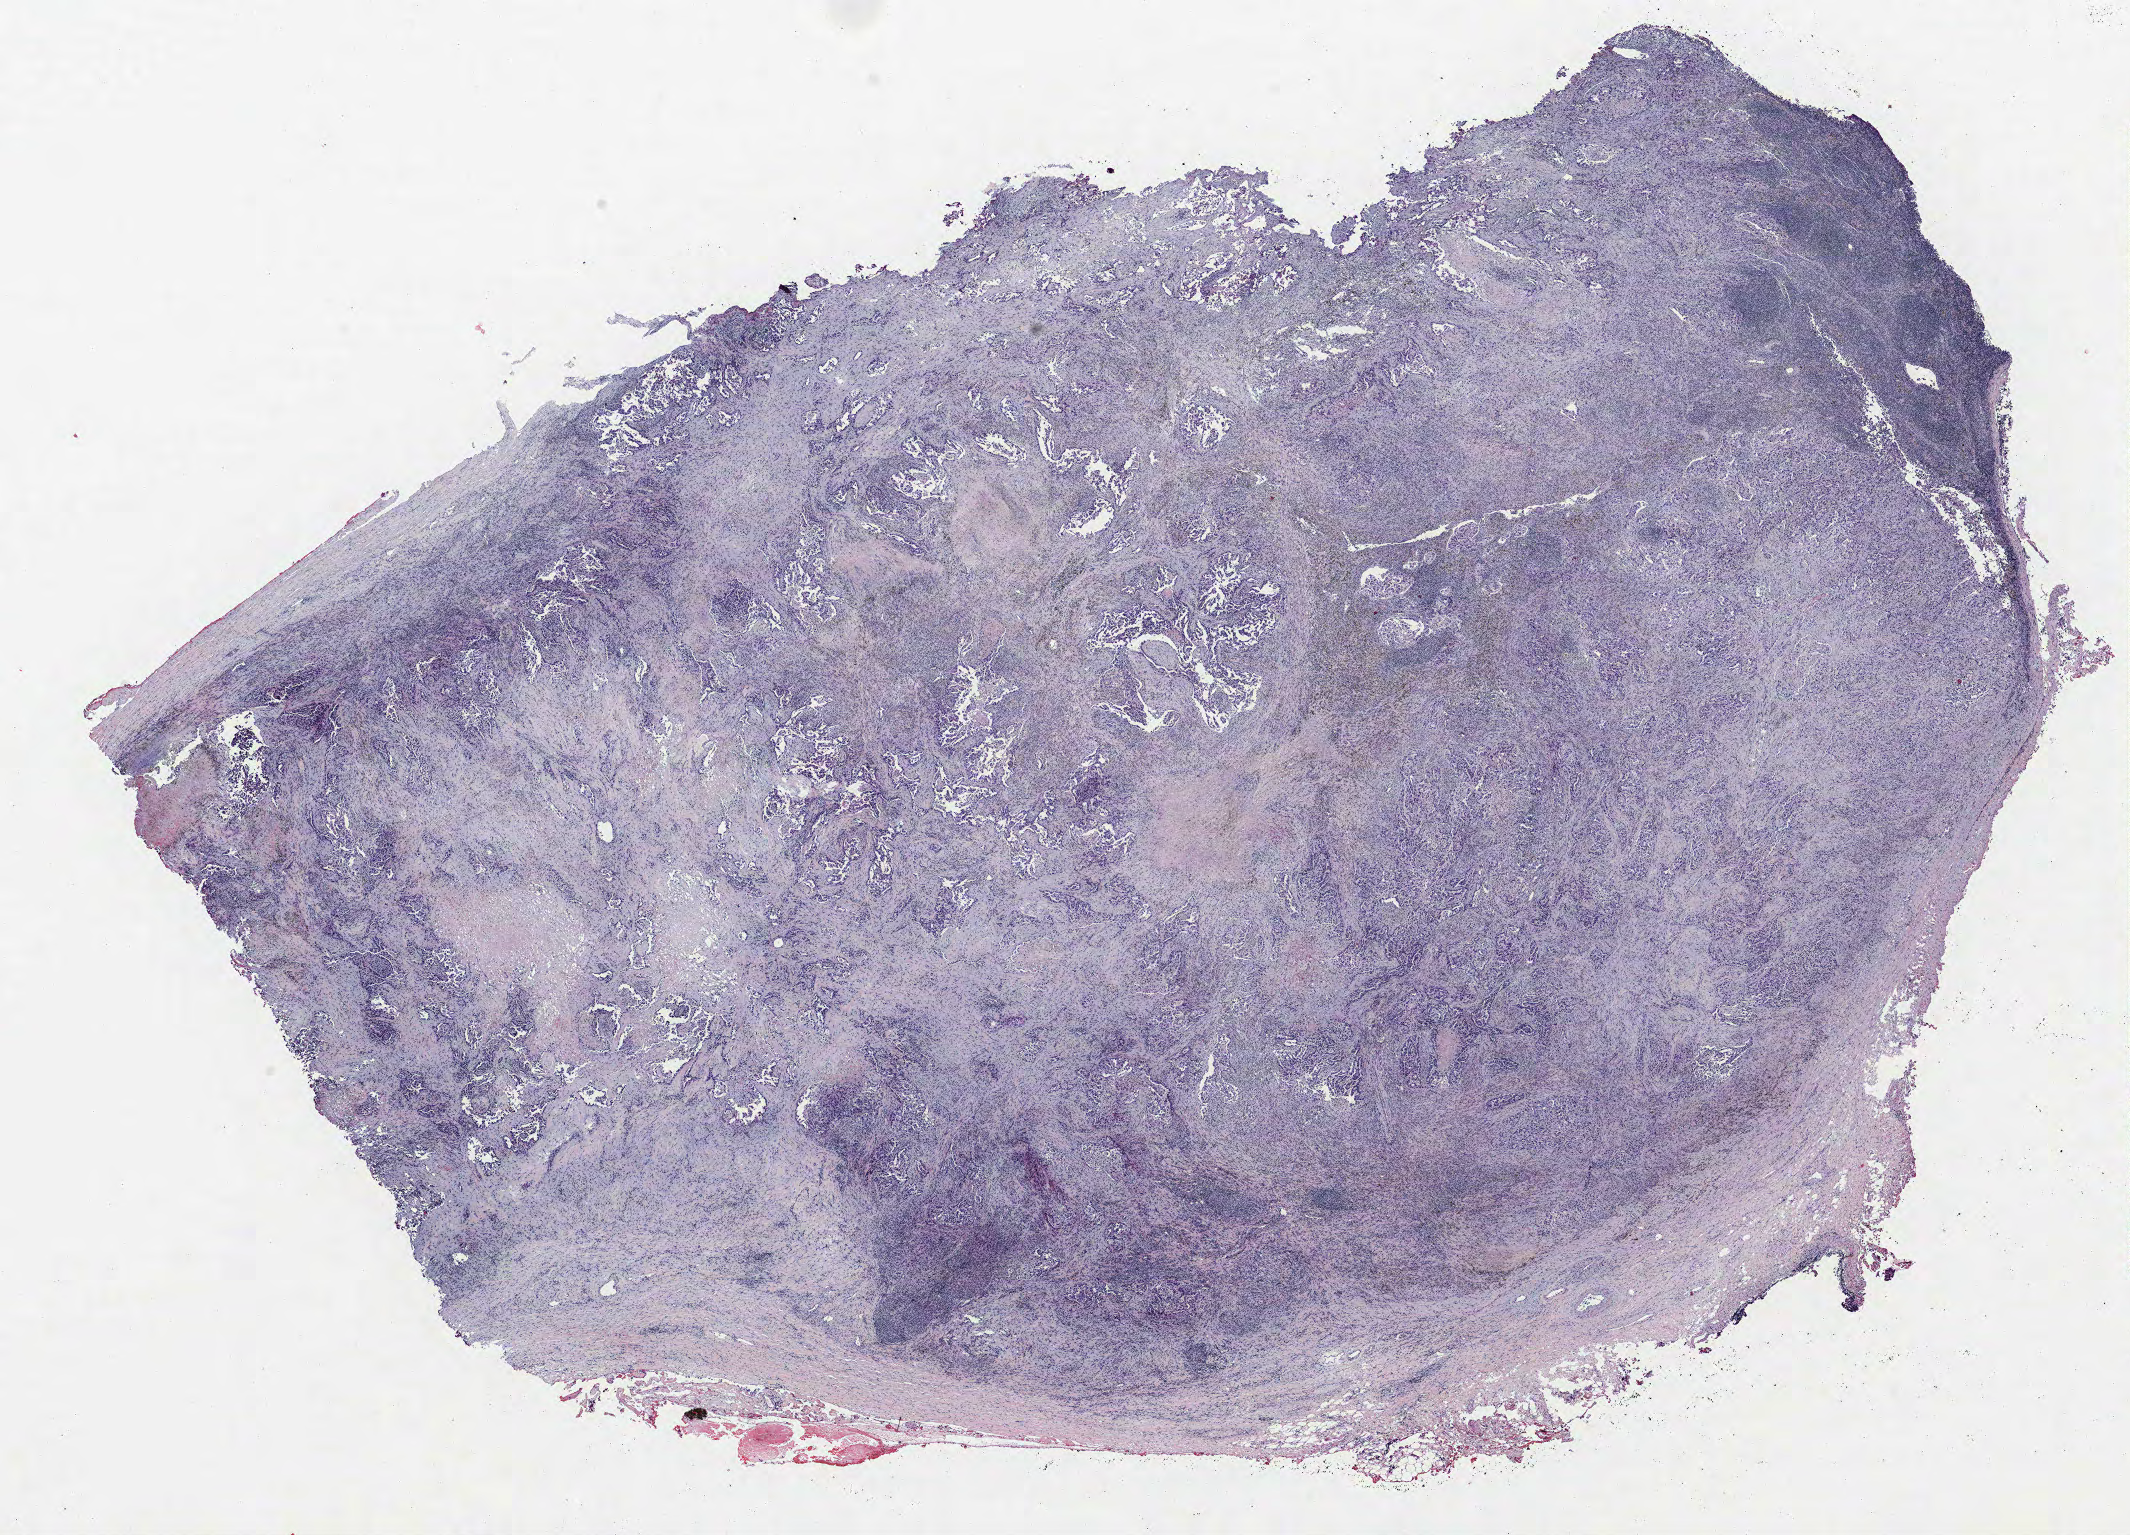
Whole-slide histology image, Hematoxylin and eosin (H&E) stained, a low-resolution overview of the entire scanned area, about 17.0 x 12.3 mm; FFPE section; lung. Male, age 73 at enrolment. Current smoker at enrolment. Grade: poorly differentiated (G3).
Tumour size (pathology): 12 mm. Primary tumour location (clinical record): left lower lobe. Participant's lung-cancer diagnosis: Adenocarcinoma, NOS (ICD-O-3 8140/3). Stage (AJCC 6th edition): IIA.